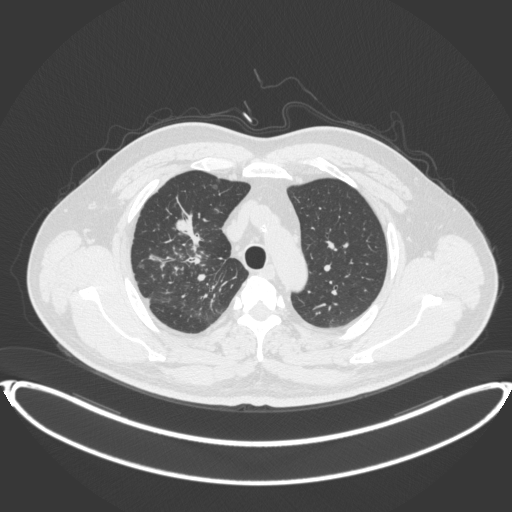
Chest CT, one axial slice; position 297 of 399 along the scan axis; reconstruction kernel B31f; 120 kVp; lung window (W 1500 / L -600 HU); 1 mm slice thickness; 512 × 512 image matrix, field of view 445 × 445 mm. Patient: male, 53 years. From the clinical record (not read from this slice): clinical TNM (as recorded): T2a N0 M0.
Structures marked on this image (bounding box drawn by a radiologist):
- lung tumour (recorded histology: adenocarcinoma): box from (x=174, y=209) to (x=205, y=247) px